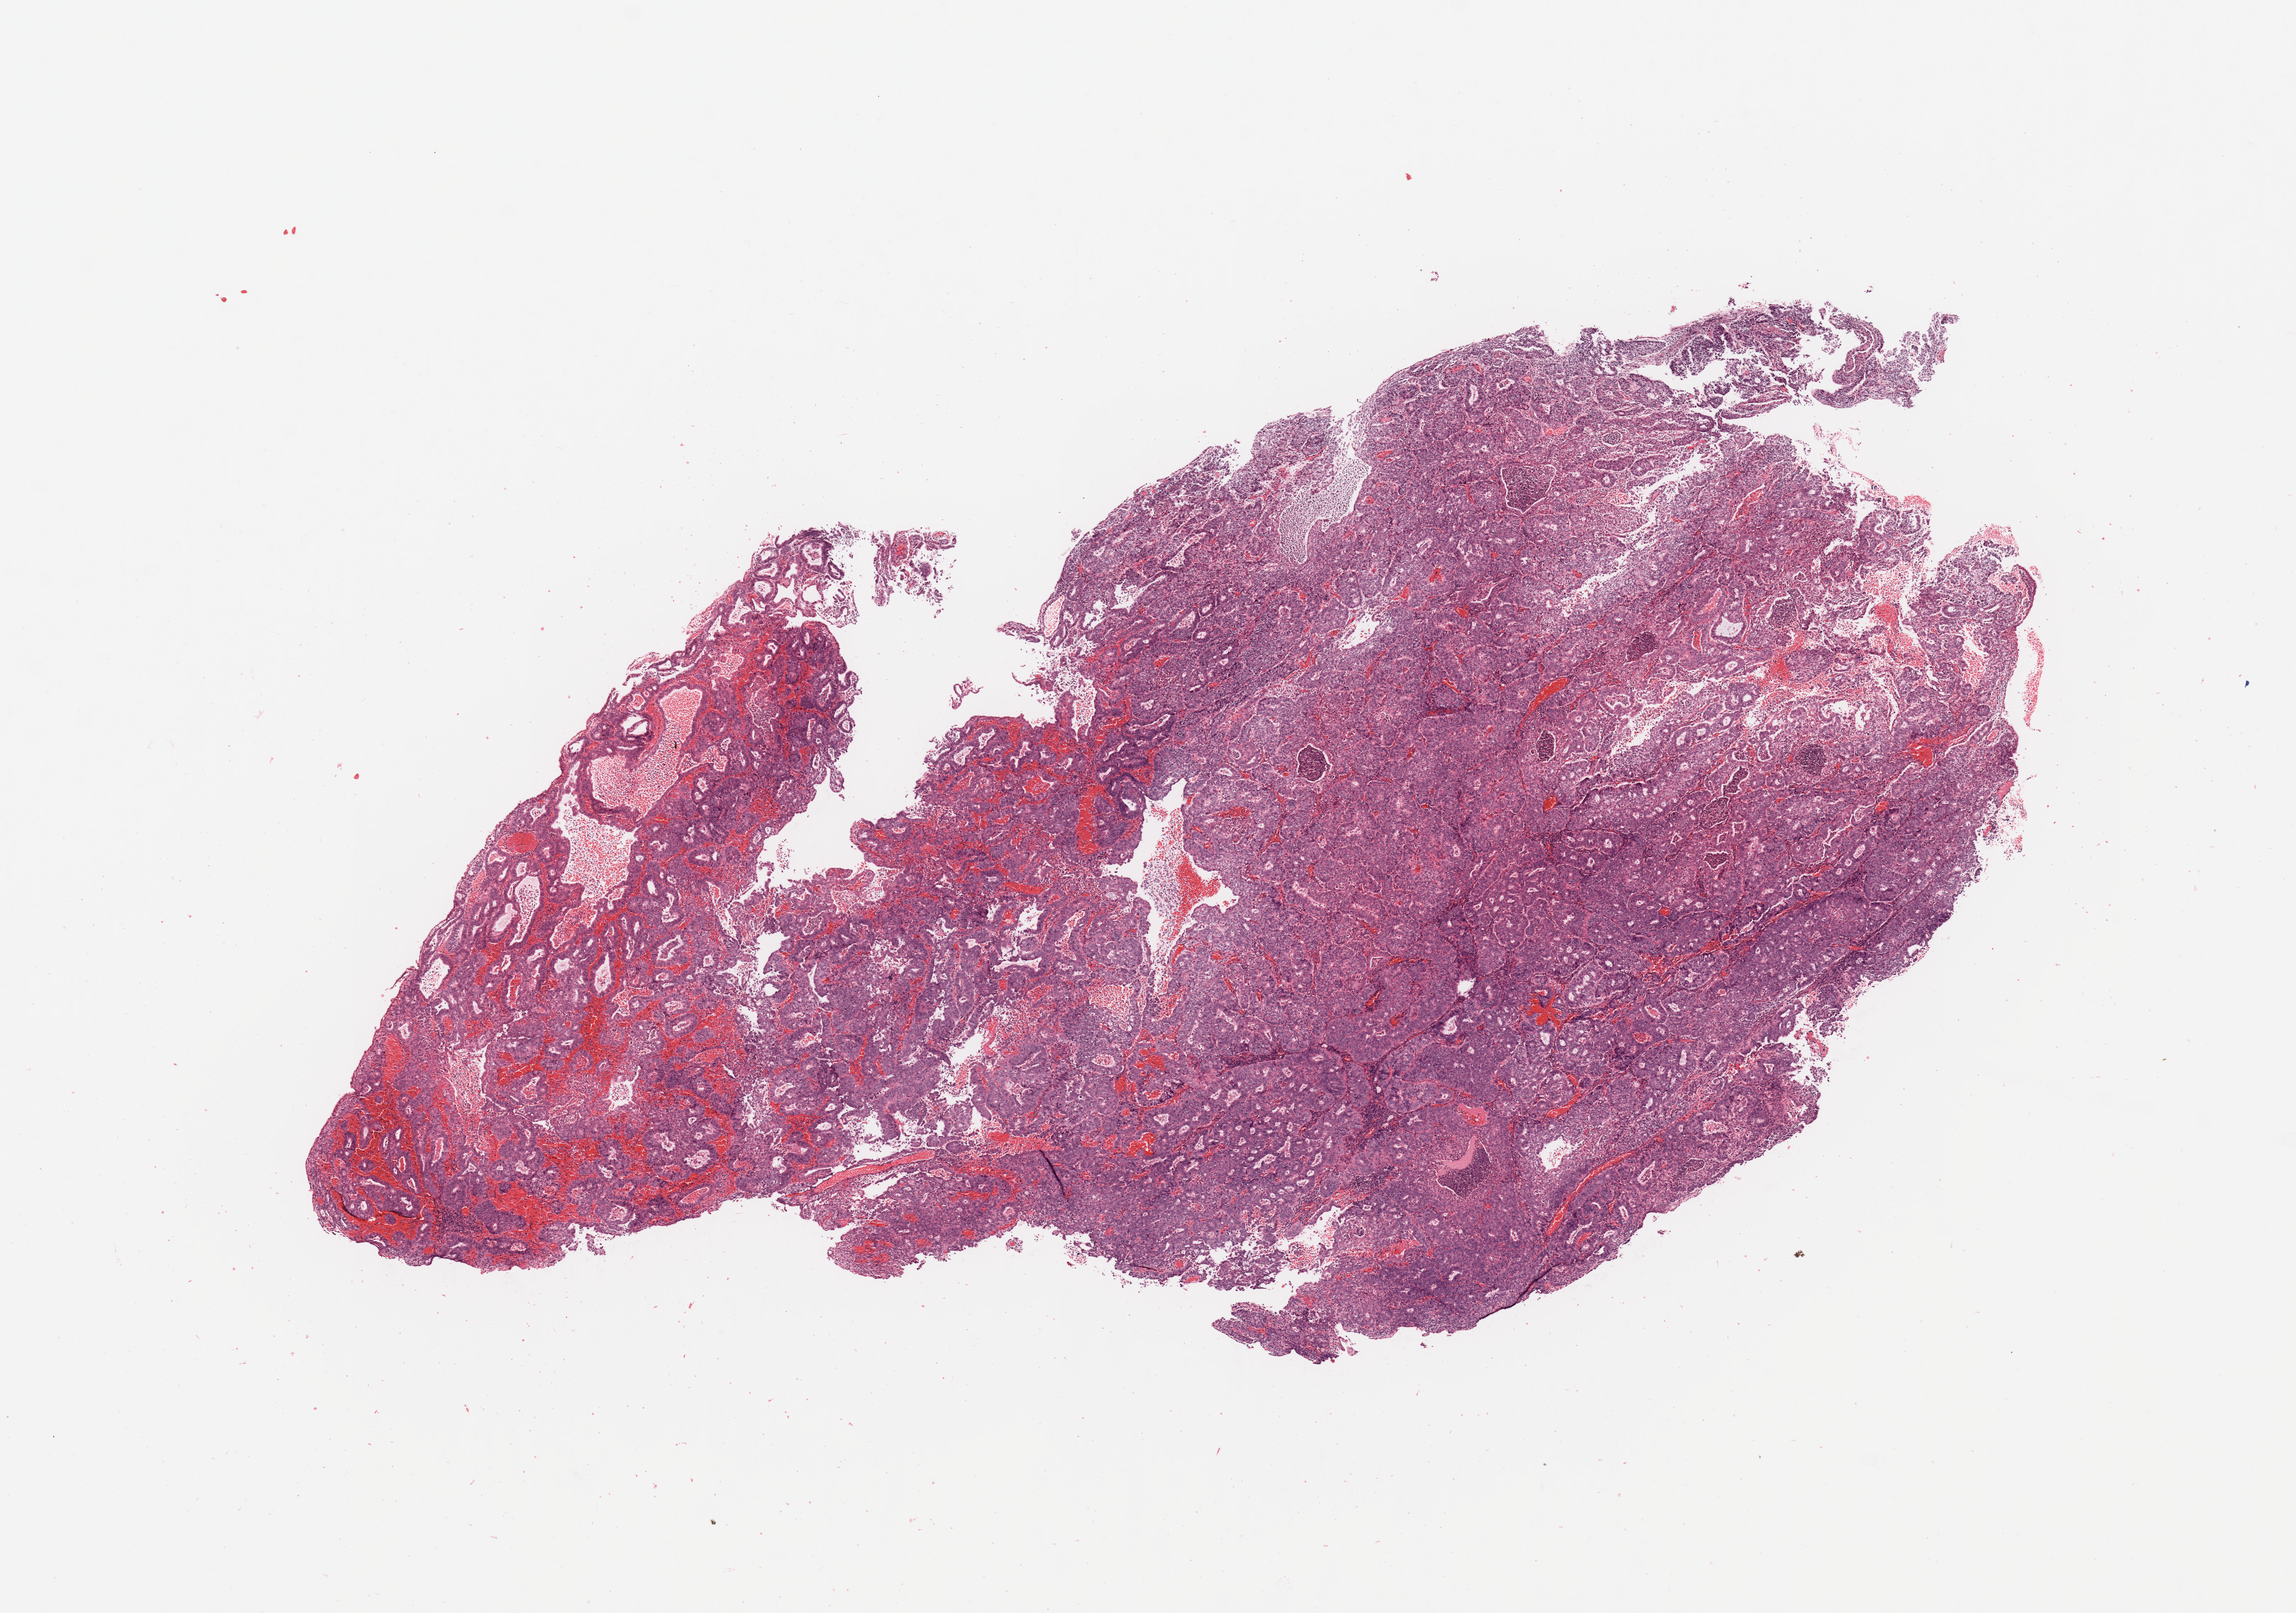
Whole-slide histology image, Hematoxylin and eosin (H&E) stained — low-resolution overview of the scanned area, about 12.8 x 9.0 mm (acquisition: 20x scan); tumour tissue sample, sampled site: uterus. 60-year-old female patient. Histologic grade: G2 (moderately differentiated). Pathologist review of this section (percent, as recorded): tumour nuclei 90%, necrosis 0%.
Histologic diagnosis: Endometrioid adenocarcinoma, NOS. AJCC pathologic stage: I.